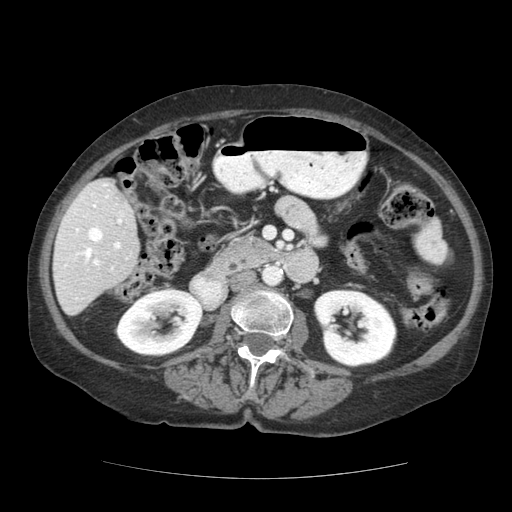
Contrast-enhanced abdominal CT (liver protocol), one axial slice. Position 53 of 111 along the scan axis. Reconstruction kernel STANDARD. 140 kVp. Soft-tissue window (W 400 / L 40 HU). 2.5 mm slice thickness. 512 × 512 image matrix. From the clinical record (not read from this slice): diagnosis: hepatocellular carcinoma (patient treated with transarterial chemoembolisation; whether this scan precedes or follows treatment is not stated here); TNM stage (as recorded): Stage-I; Child-Pugh class: A; tumour differentiation: moderately-poorly differentiated; tumour nodularity: uninodular.
Annotated regions visible in this slice (semi-automatic segmentation, software-assisted and operator-edited):
- liver parenchyma outside the tumour (the mass and vessels are separate outlines, so this box may not span the whole liver): bounding box (x1, y1, x2, y2) in pixels: (52, 178, 140, 314)
- liver vessels: (59, 184, 128, 269)